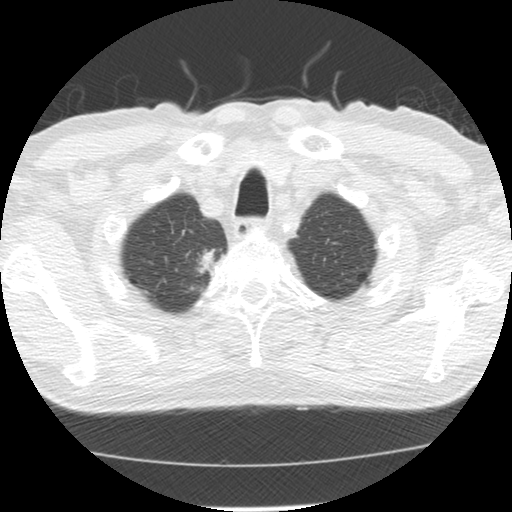
Low-dose screening chest CT, one axial slice; reconstruction kernel STANDARD; lung window (W 1500 / L -600 HU); 2.5 mm slice thickness; 512 × 512 image matrix, field of view 310 × 310 mm.
Annotated regions visible in this slice (expert manual segmentation):
- lesion 1 (tumor, upper lobe of right lung): bounding box [x1, y1, x2, y2] px = [196, 249, 216, 276]